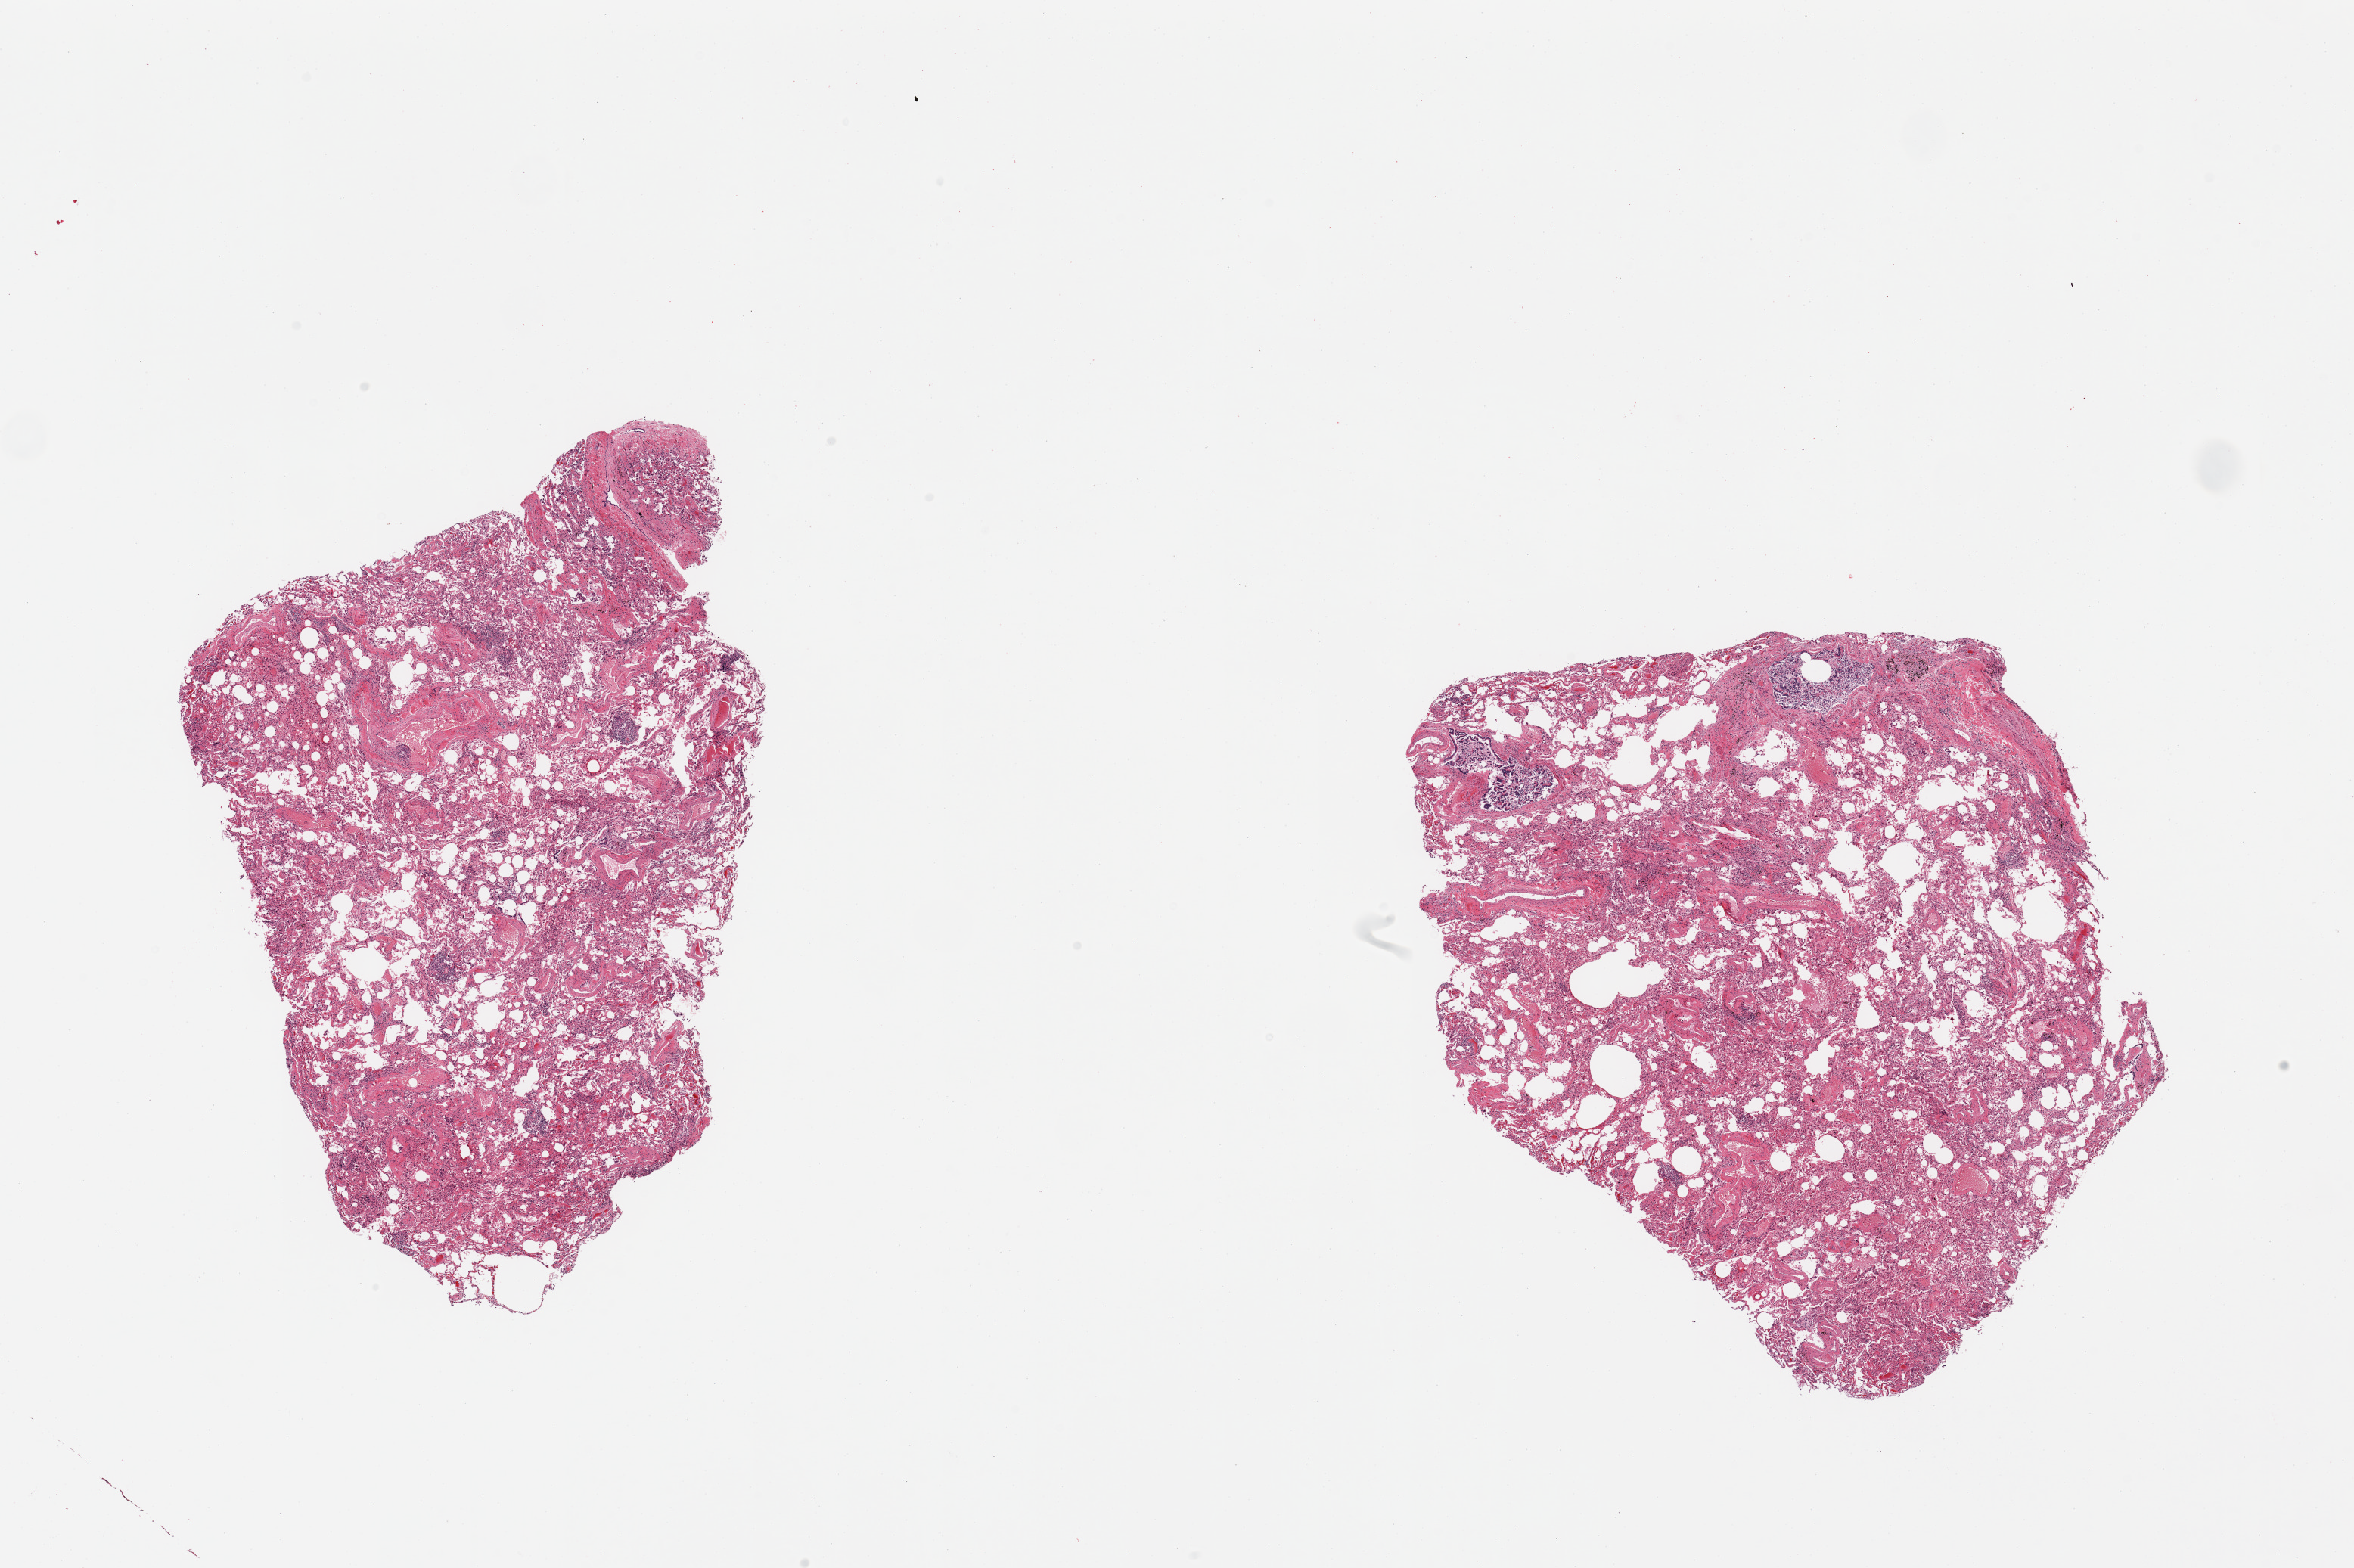
Digitized H&E-stained section, brightfield — shown as a low-resolution overview of the whole scanned area (about 24.6 x 16.4 mm, from a 20x scan); PAXgene-fixed, paraffin-embedded tissue; target tissue: lung; tissue donor sample. Donor: male.
Review note (as recorded): 2 pieces; congestion, emphysema-like changes, thickened alveolar walls and atelectasis; sloughed bronchial epithelium; one piece contains several noncaseating granulomata with foreign-body type giant cells.